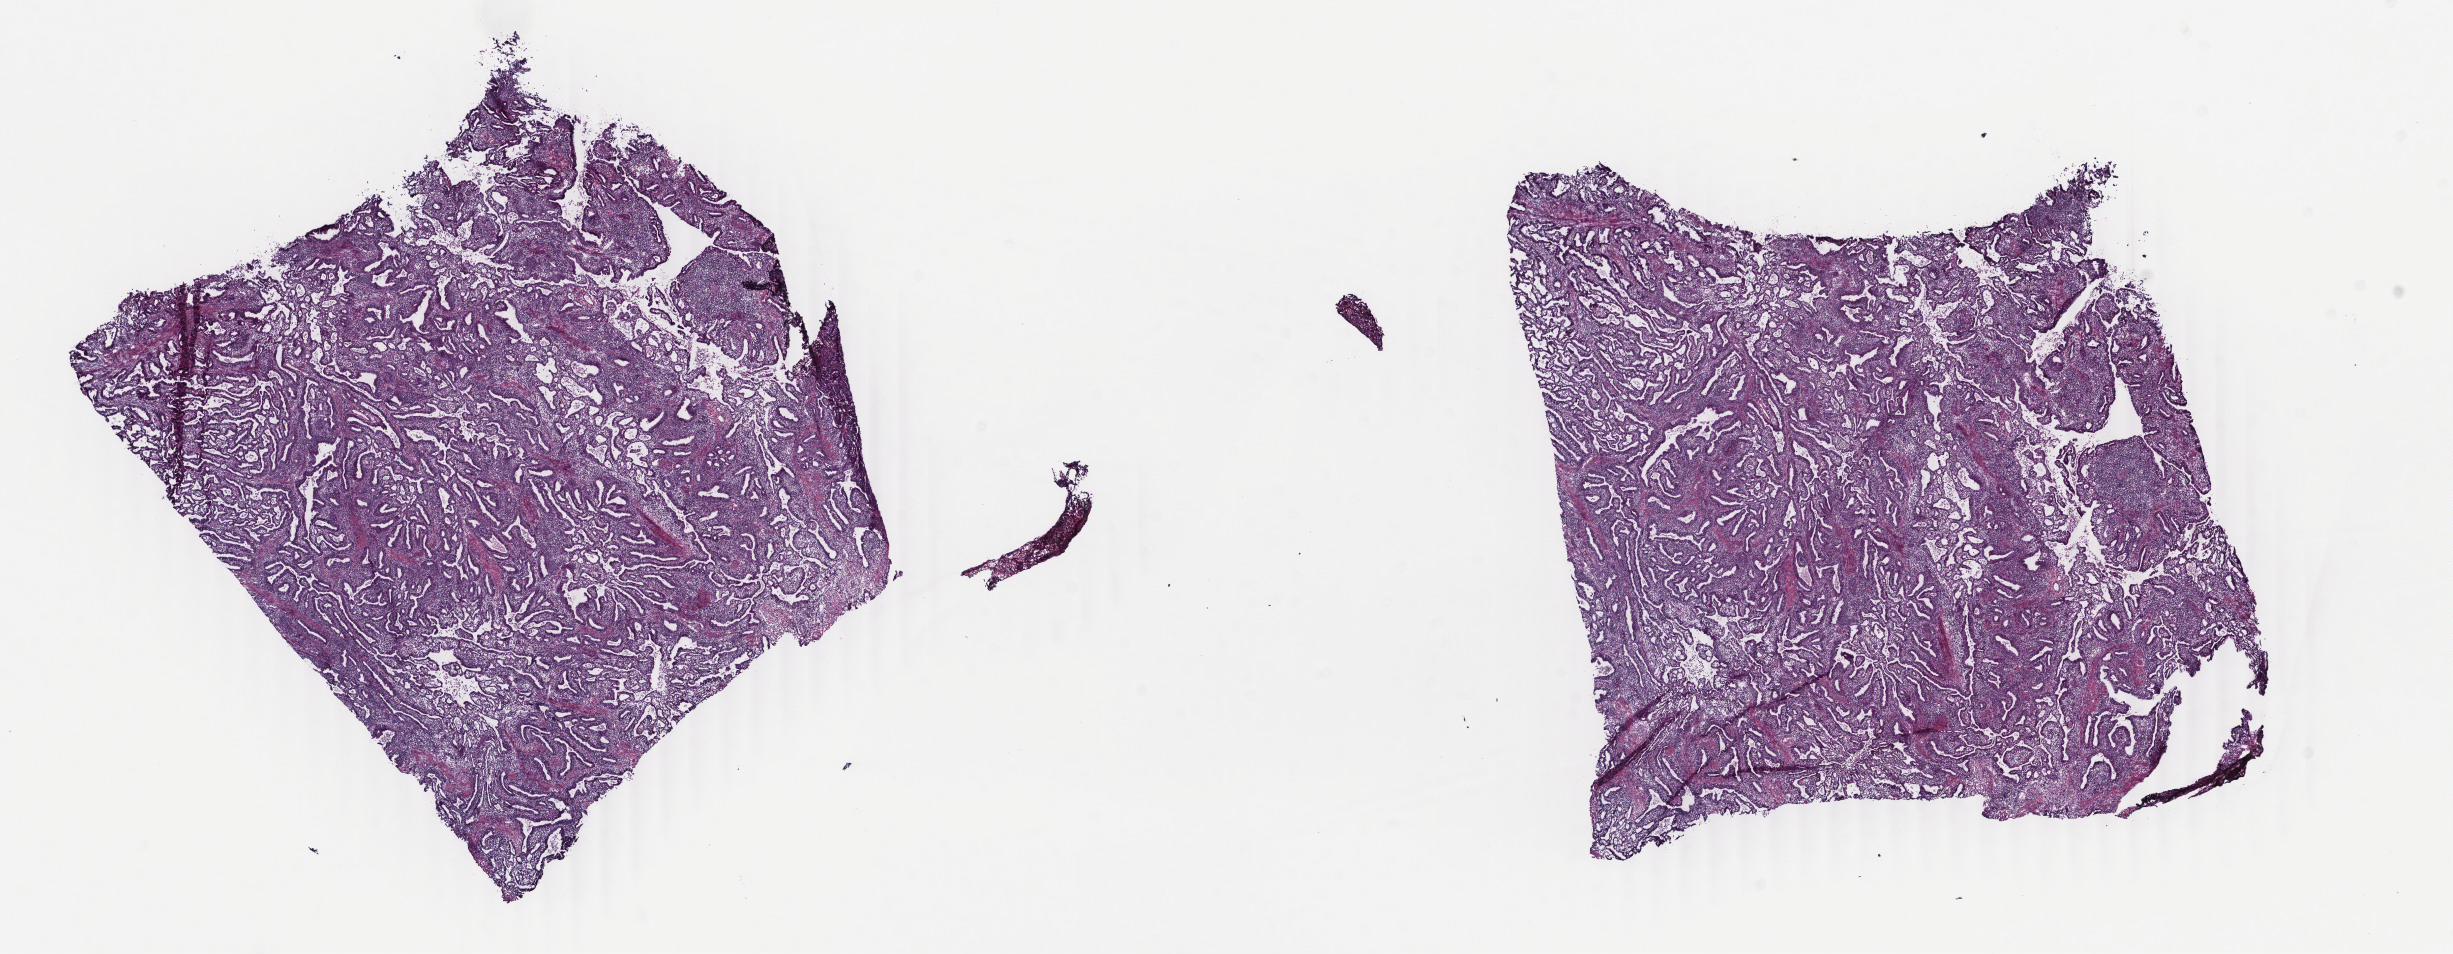
Digitized H&E-stained tissue section (whole slide), shown as a low-resolution overview of the whole scanned area (about 19.5 x 7.6 mm, slide scanned at 40x). Frozen section from the top of the tissue portion. Uterus, primary tumour sample. Female patient; age at initial diagnosis 61 years. Histologic grade: G2 (moderately differentiated). Pathologist review of this section (percent, as recorded): tumour cells 80%, tumour nuclei 65%, normal cells 0%, stromal cells 20%, necrosis 0%. Inflammatory infiltration, as recorded: lymphocyte infiltration 0%, monocyte infiltration 0%, neutrophil infiltration 0%.
Diagnosis: Endometrioid adenocarcinoma, NOS. FIGO stage: IIB.